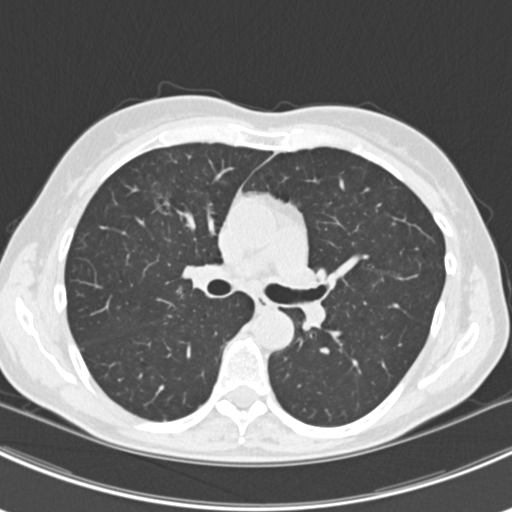
Axial slice from a low-dose chest CT screening exam; baseline screening round; lung window (W 1500 / L -600 HU); slice 75 of 224 in the series; 512 × 512 image matrix, field of view 310 × 310 mm. Female participant, aged 63 years at enrolment. Current smoker at enrolment.
- Expert-annotated lung lesion, bounding box [x1, y1, x2, y2] px = [144, 180, 201, 236].
- The screening reader recorded 10 non-calcified nodules or masses ≥4 mm on this exam (right lower lobe, right lower lobe, left lower lobe, left lower lobe, right middle lobe, right lower lobe, left lower lobe, left upper lobe, right upper lobe, left upper lobe); which of them this box marks is not recorded.
- Later outcome: lung cancer diagnosed 751 days after this screen (after the third annual screen) — bronchiolo-alveolar adenocarcinoma, NOS, right upper lobe, right middle lobe, right lower lobe, left upper lobe, left lower lobe, moderately differentiated (G2), stage IV (AJCC 6th edition).